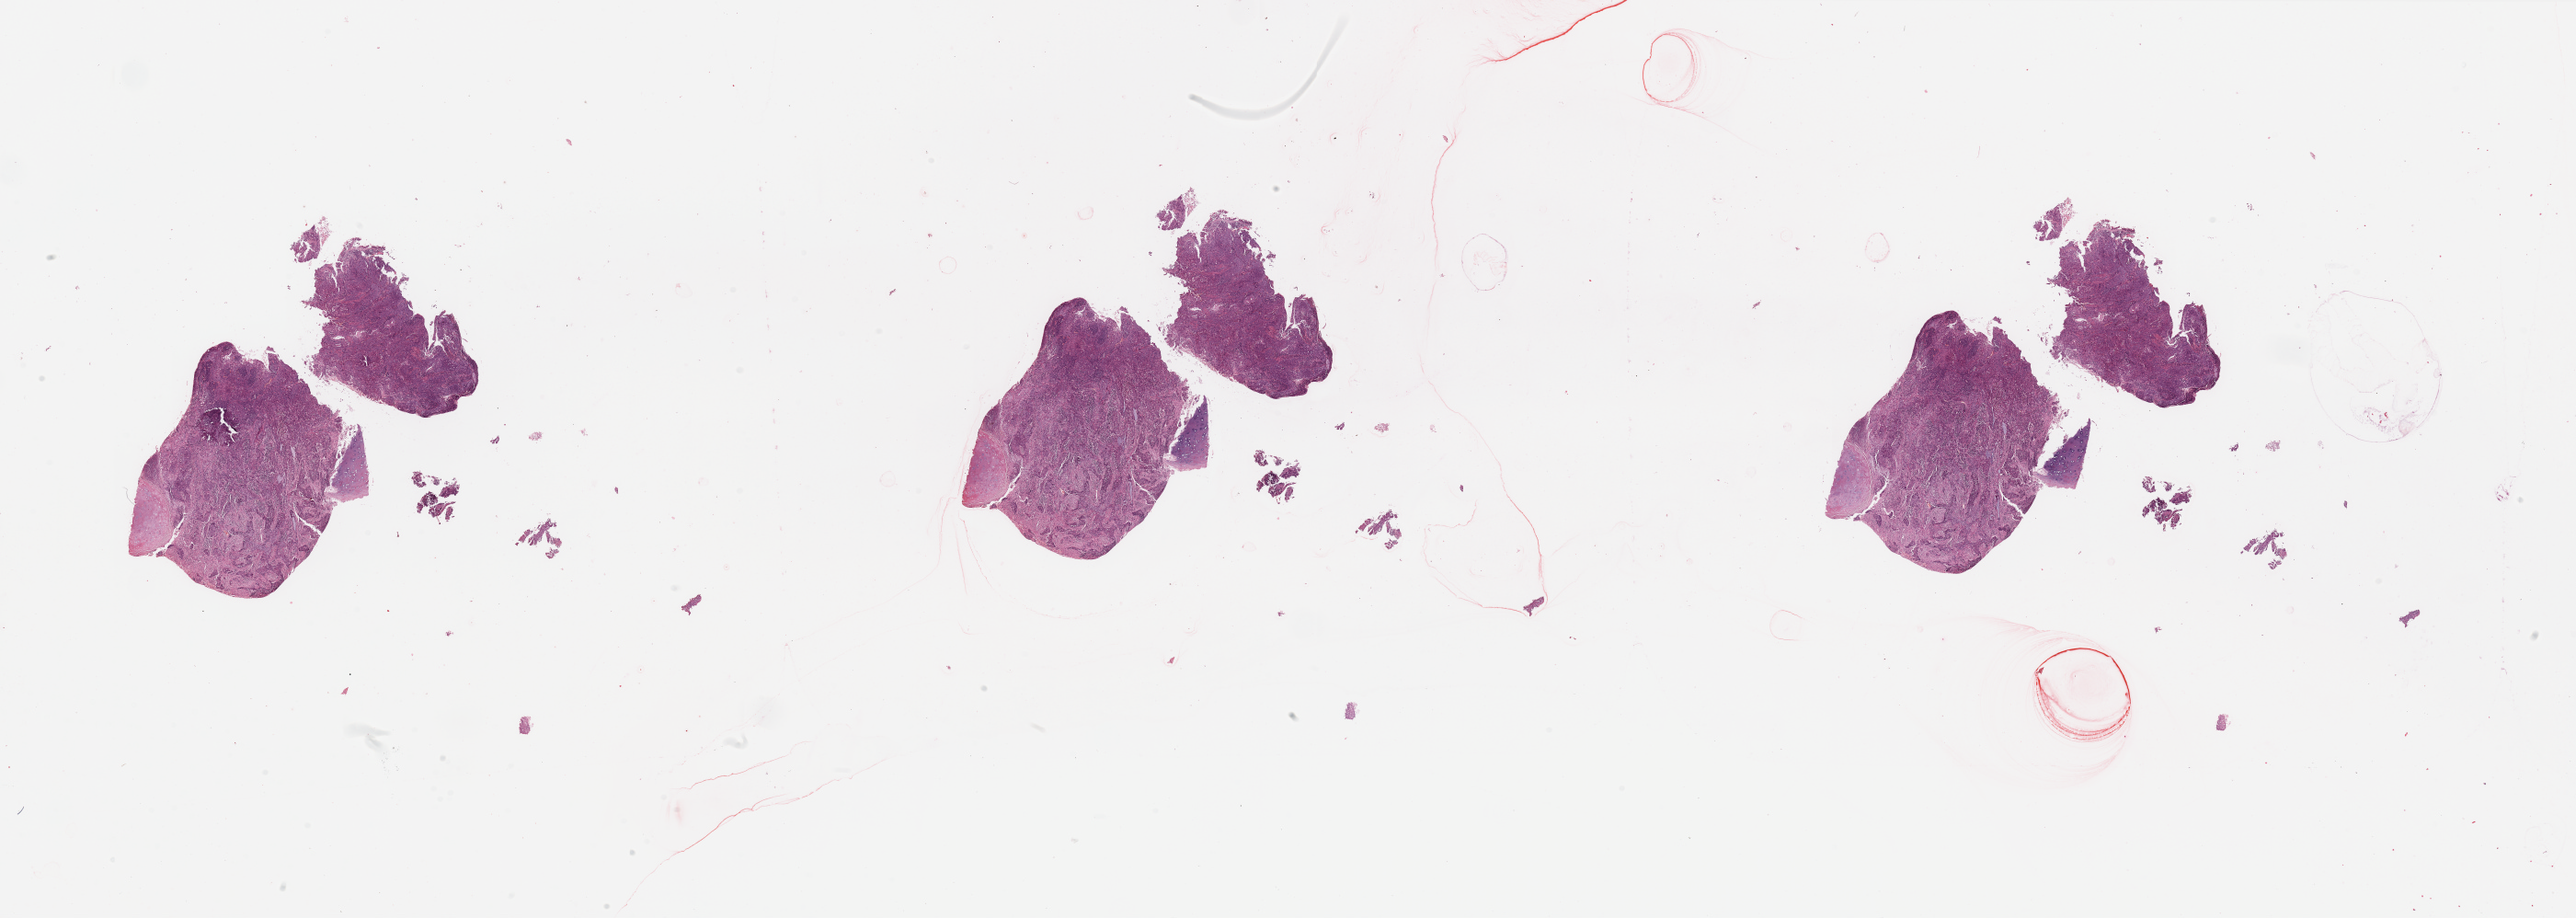
Whole-slide histology image, H&E — shown as a low-resolution overview of the whole scanned area (about 44.3 x 15.8 mm, acquisition: 20x scan), tumour tissue sample, sampled site: lung. Male, 73 y/o. Histologic grade: G2 (moderately differentiated). Slide review estimates, as recorded: tumour nuclei 80%, necrosis 2%.
AJCC pathologic stage: II. Primary tumour site (as recorded): right middle lobe. Histologic diagnosis: Squamous cell carcinoma, NOS.